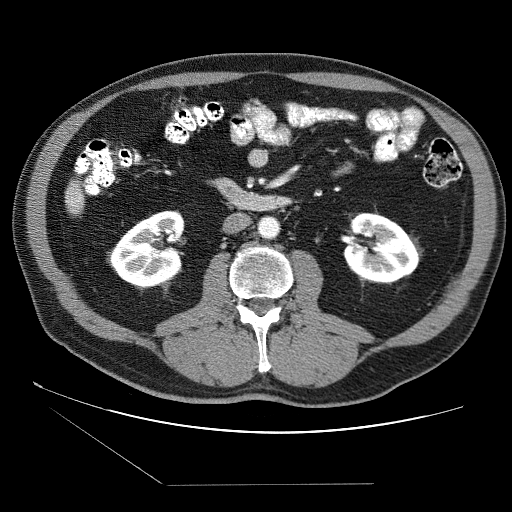
Contrast-enhanced abdominal CT (liver protocol), one axial slice; position 5 of 87 along the scan axis; soft-tissue window (W 400 / L 40 HU); 2.5 mm slice thickness; 512 × 512 image matrix, field of view 400 × 400 mm. From the clinical record (not read from this slice): diagnosis: hepatocellular carcinoma (patient treated with transarterial chemoembolisation; whether this scan precedes or follows treatment is not stated here); TNM stage (as recorded): Stage-II; Child-Pugh class: B; tumour differentiation: no biopsy; tumour nodularity: multinodular.
Outlined on this slice (semi-automatic segmentation, software-assisted and operator-edited):
- liver parenchyma outside the tumour (the mass and vessels are separate outlines, so this box may not span the whole liver): bounding box [x1, y1, x2, y2] px = [65, 180, 84, 214]
- liver vessels: [73, 195, 81, 204]